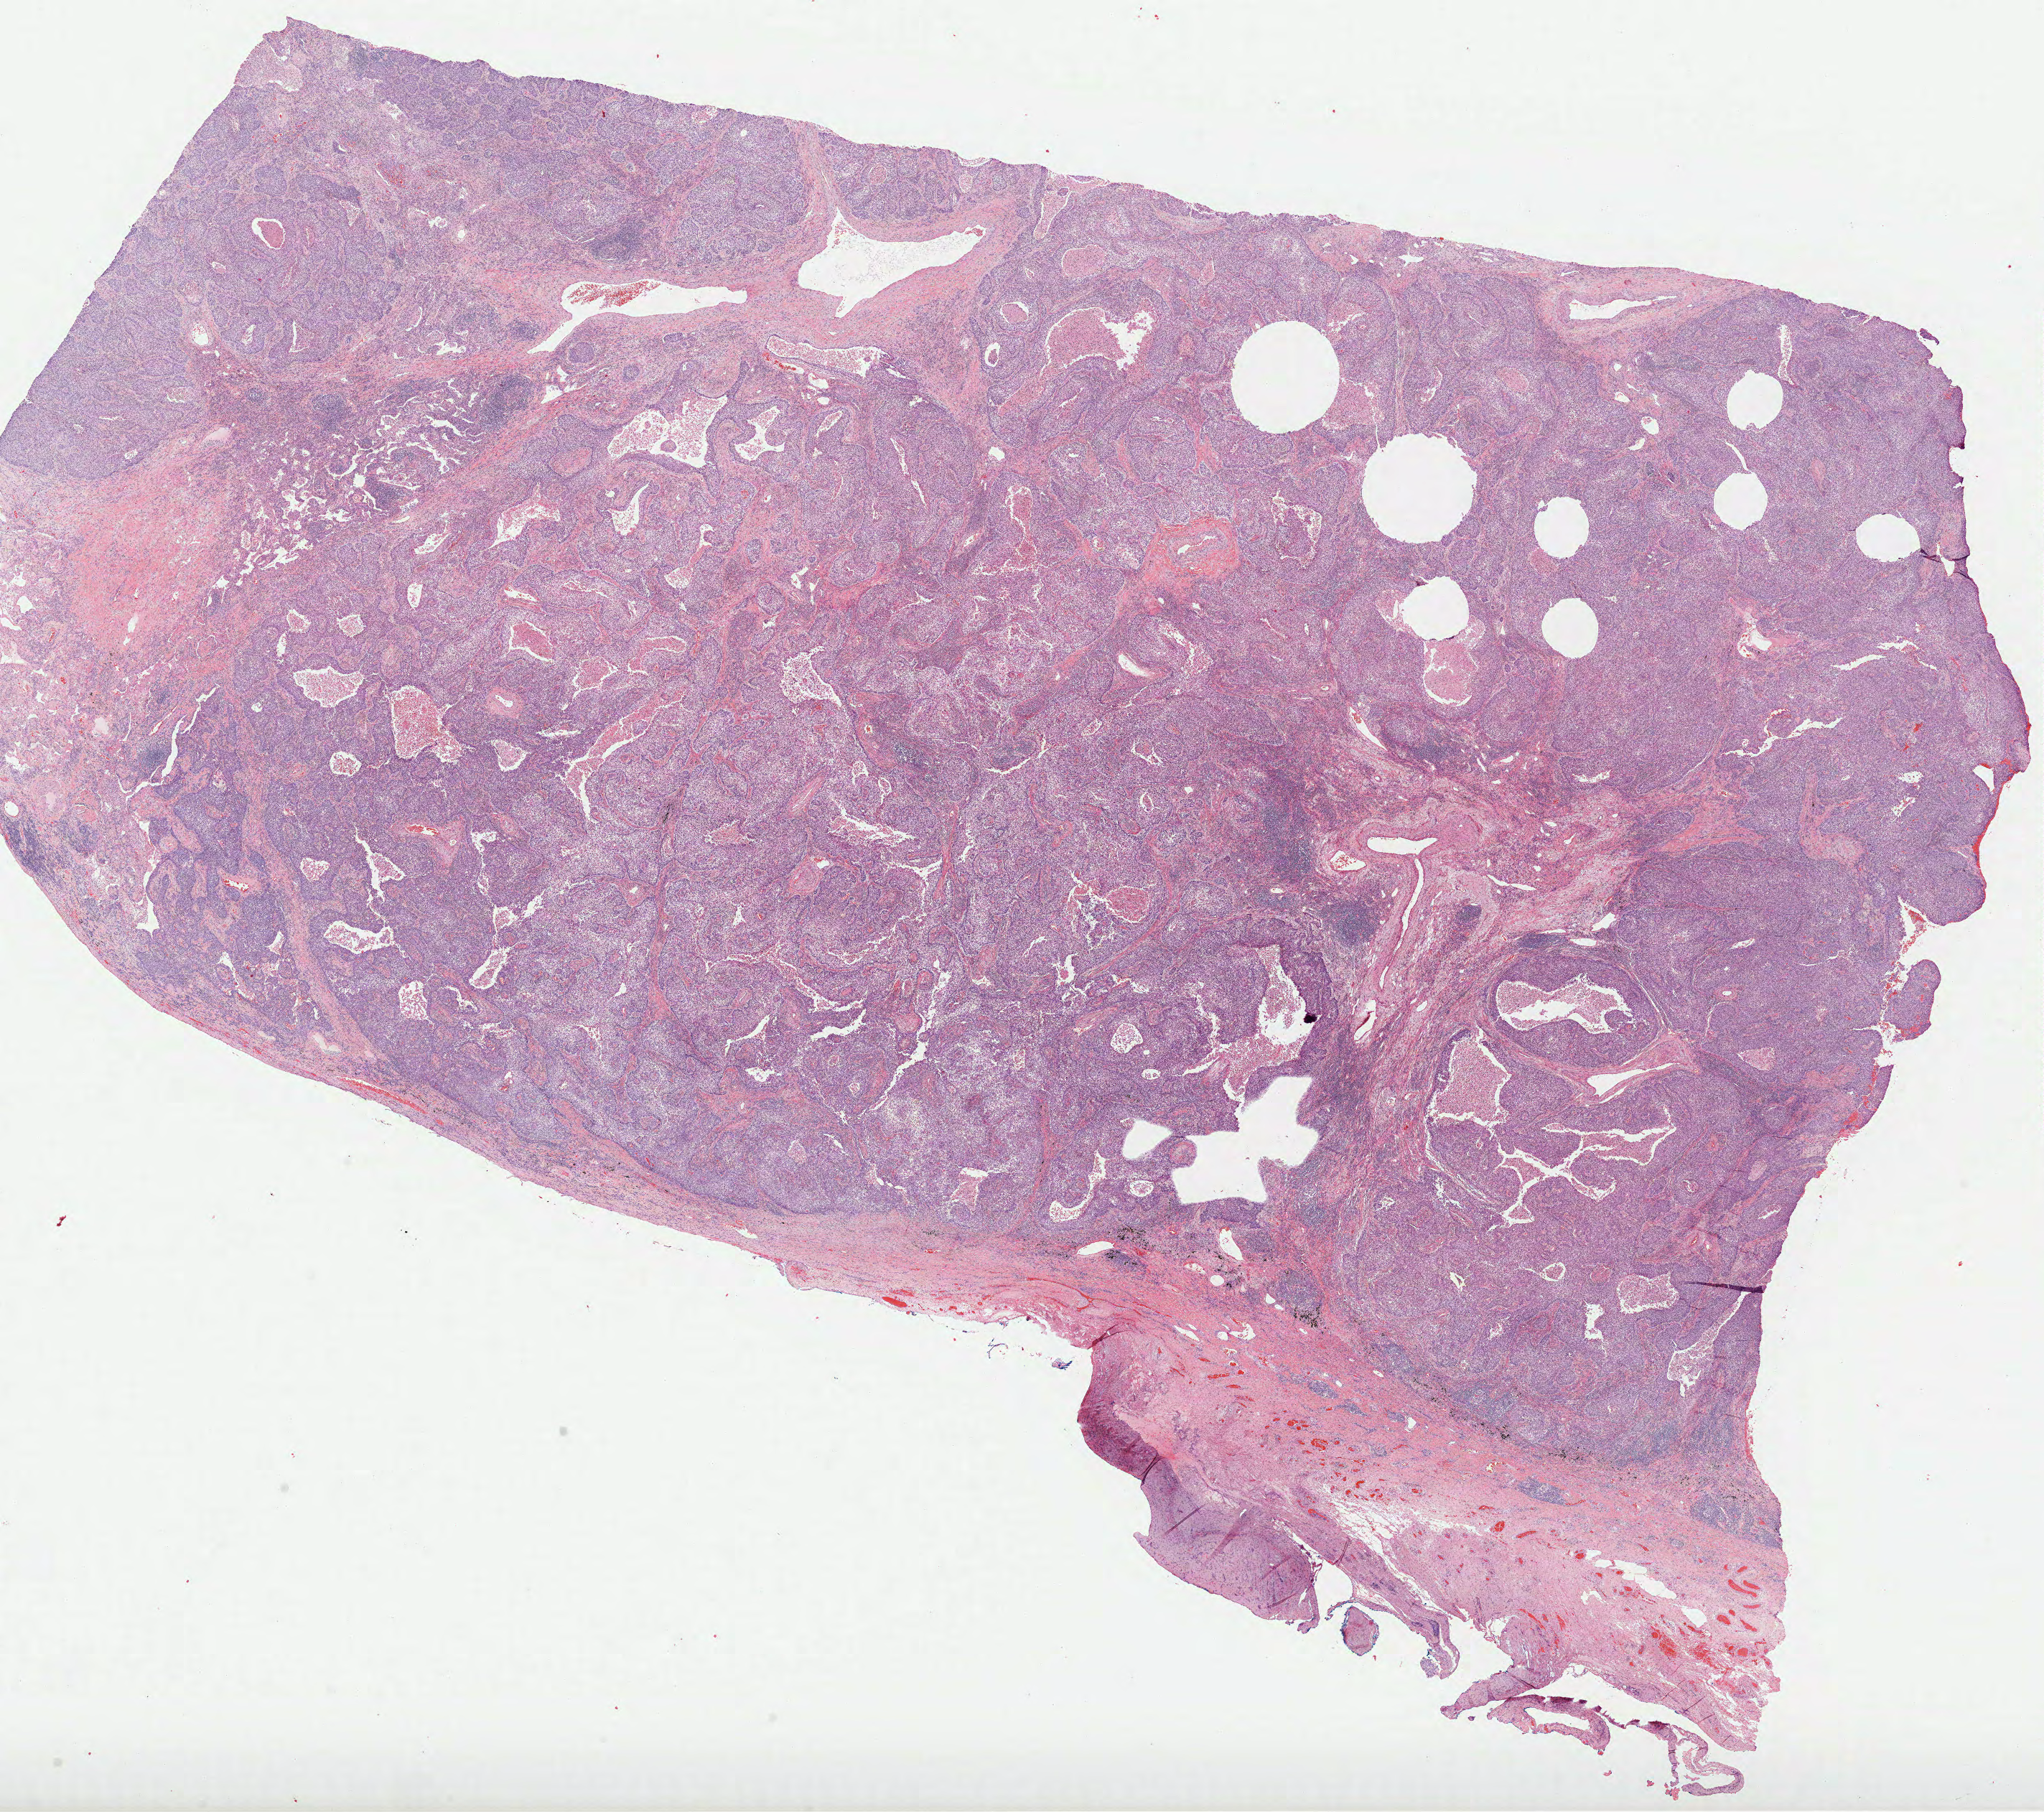
H&E whole-slide image, low-resolution overview of the scanned area, about 23.0 x 20.4 mm (from a 40x scan). Formalin-fixed paraffin-embedded (FFPE) diagnostic section. Primary tumour sample from the lung. Female, age 64 years at initial diagnosis.
Histologic diagnosis: Squamous cell carcinoma, NOS. AJCC pathologic stage: IB.